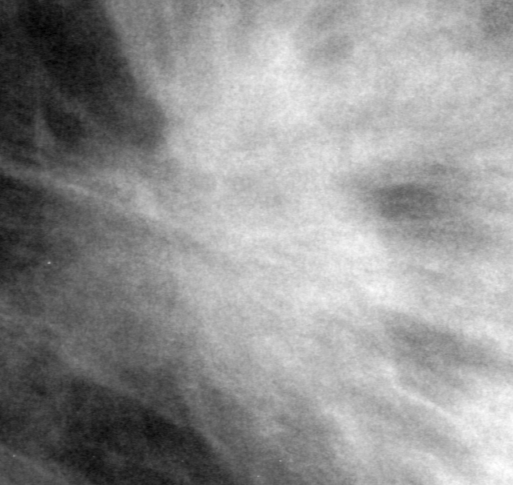
Region of interest cut from a scanned film mammogram (one marked finding); right breast; MLO view.
Finding: mass, shape irregular, margins spiculated; BI-RADS assessment category 5; subtlety rating 4 on a 1 (subtle) to 5 (obvious) scale; pathology (as recorded): malignant.